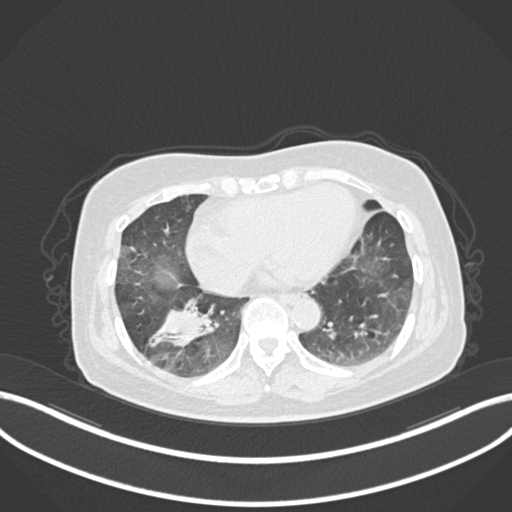
Chest CT, one axial slice. Position 41 of 222 along the scan axis. Lung window (W 1500 / L -600 HU). 1 mm slice thickness. 512 × 512 image matrix, field of view 400 × 400 mm. Patient: female, 67 years. From the clinical record (not read from this slice): clinical TNM (as recorded): T1c N1 M0; histopathological grade: G2-3.
Annotated regions visible in this slice (bounding box drawn by a radiologist):
- lung tumour (recorded histology: adenocarcinoma): bounding box <144,294,223,355> (left, top, right, bottom; pixels)